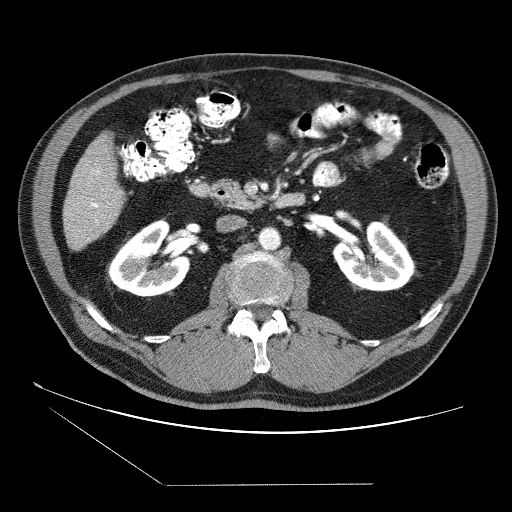
Contrast-enhanced abdominal CT (liver protocol), one axial slice. Slice 15 of 87 in the series (ordered by position). Reconstruction kernel STANDARD. Soft-tissue window (W 400 / L 40 HU). 2.5 mm slice thickness. 512 × 512 image matrix. From the clinical record (not read from this slice): diagnosis: hepatocellular carcinoma (patient treated with transarterial chemoembolisation; whether this scan precedes or follows treatment is not stated here); TNM stage (as recorded): Stage-II; Child-Pugh class: B; tumour size: 2.6 cm.
Outlined on this slice (semi-automatic segmentation, software-assisted and operator-edited):
- liver parenchyma outside the tumour (the mass and vessels are separate outlines, so this box may not span the whole liver): bounding box [x1, y1, x2, y2] px = [64, 134, 124, 250]
- liver vessels: [90, 169, 112, 208]